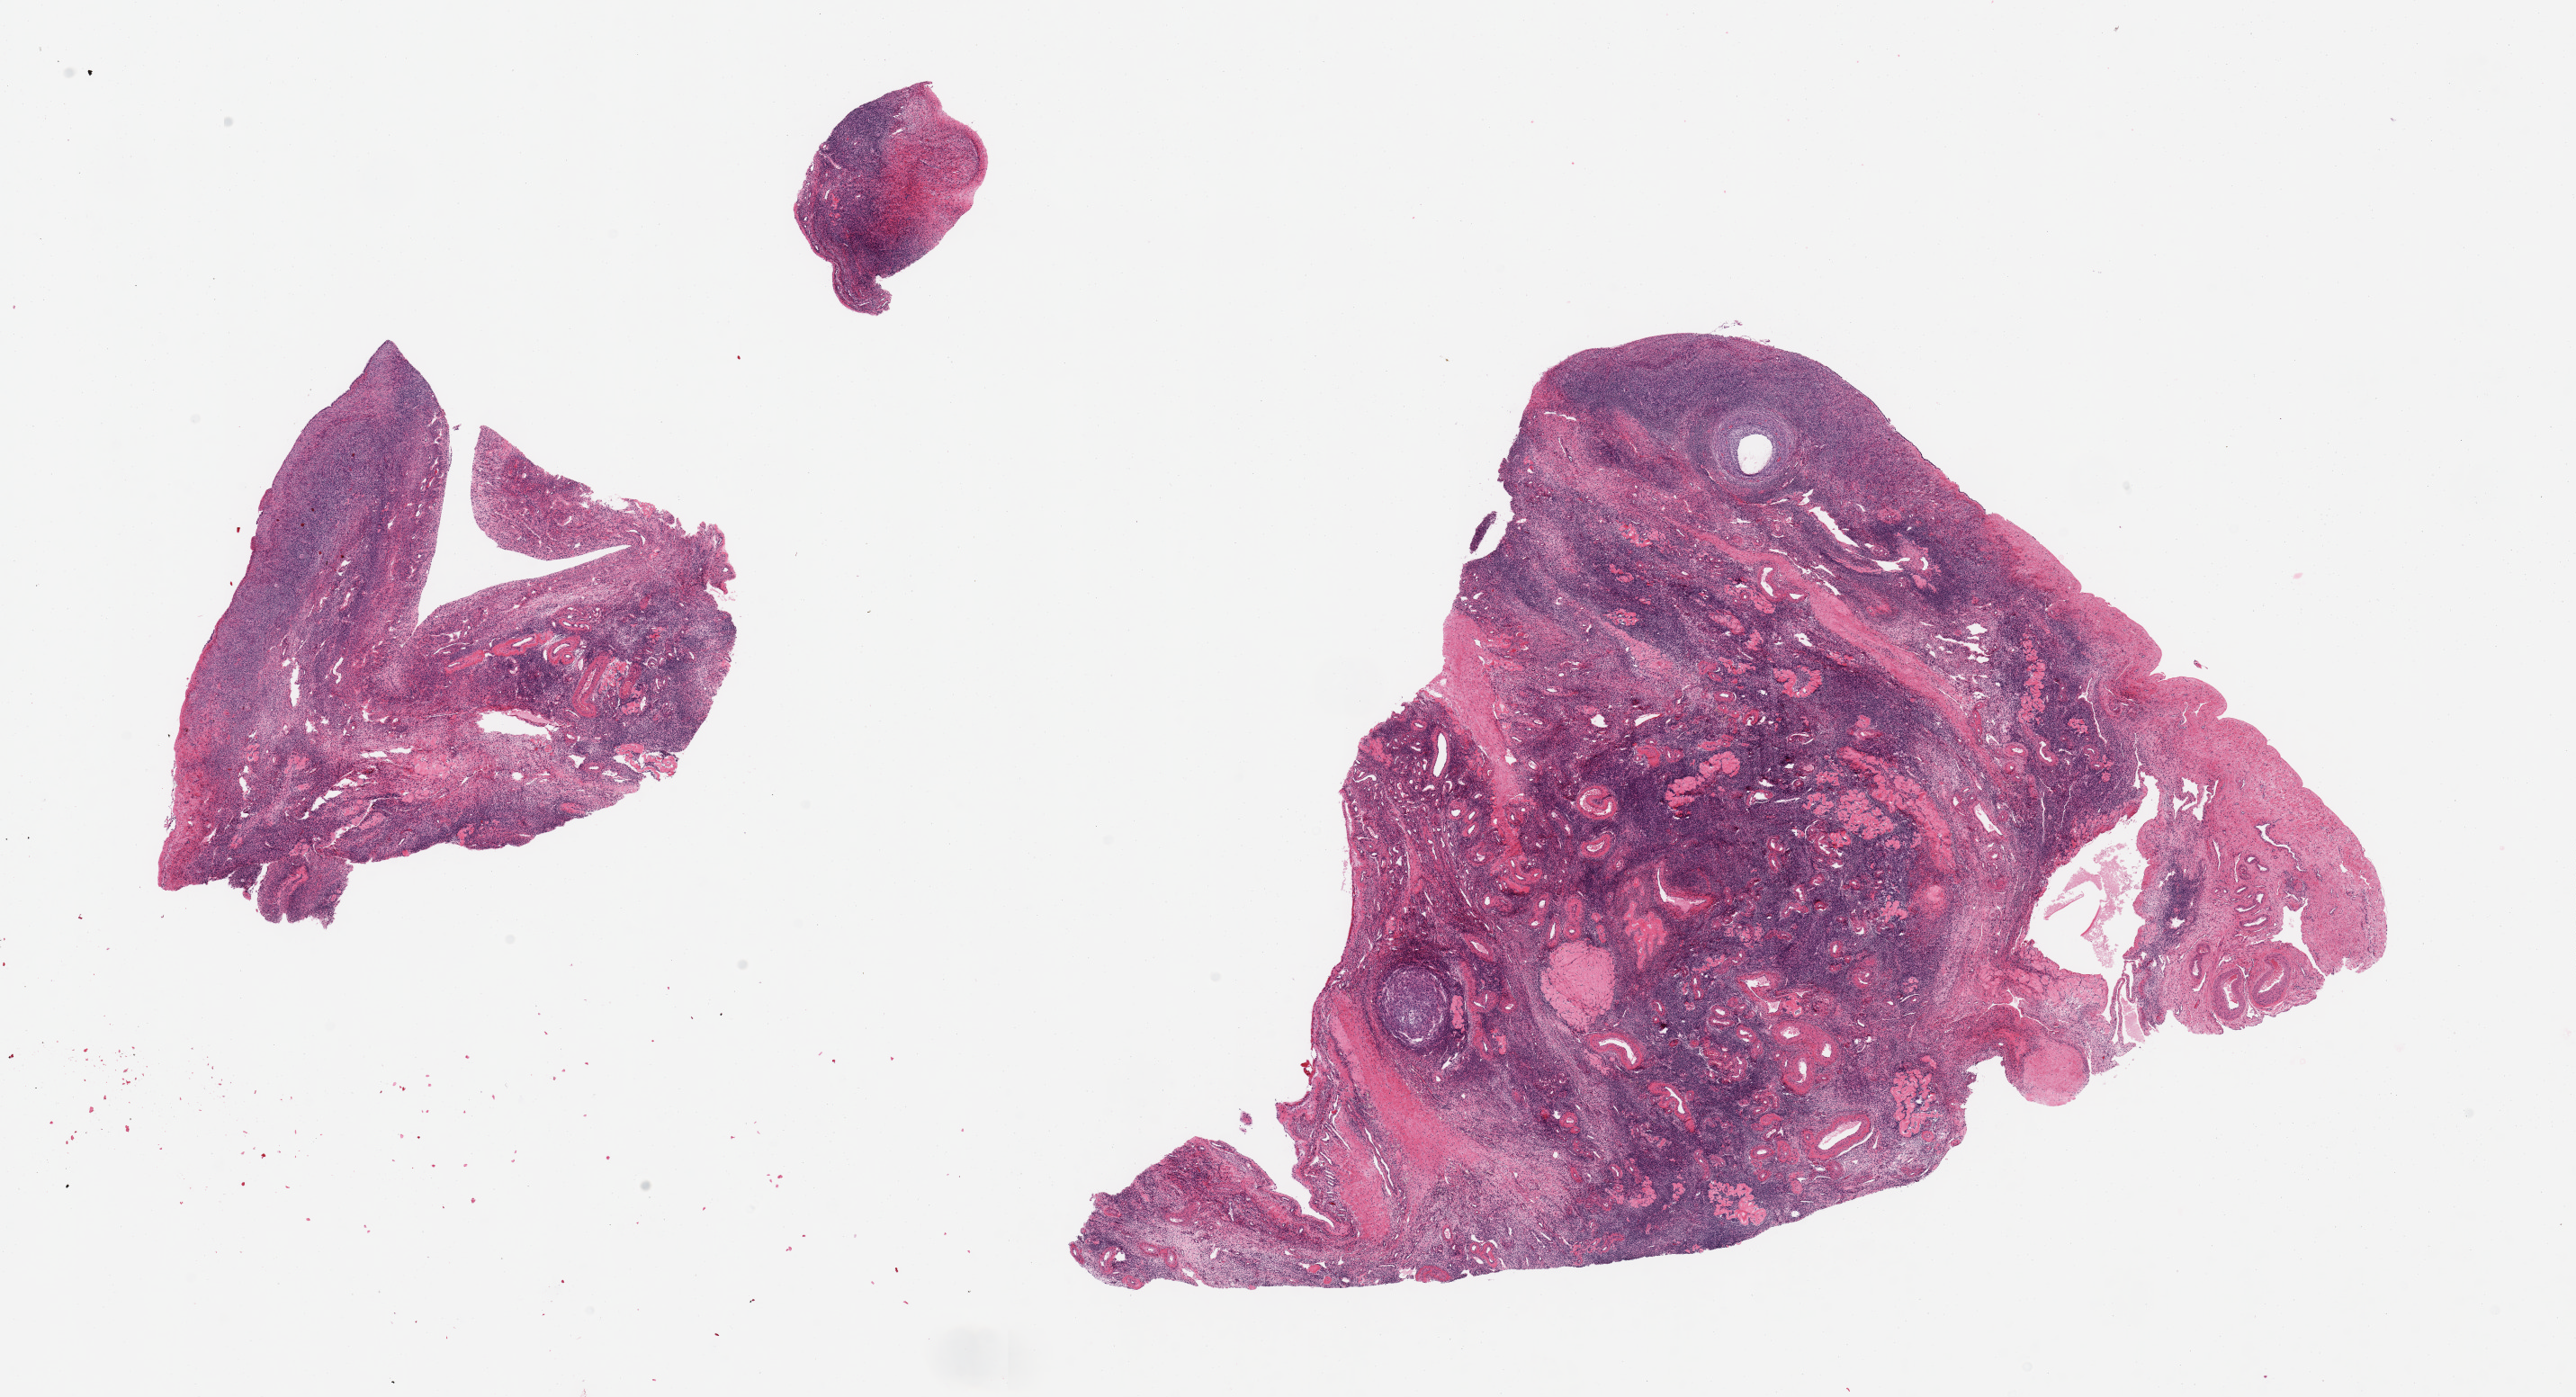
Digitized hematoxylin and eosin (H&E)-stained section — whole scanned area (about 22.6 x 12.3 mm) shown as a low-resolution overview; PAXgene-fixed, paraffin-embedded tissue; sampled site (target tissue): ovary; donor tissue sample. Donor sex: female.
Pathologist's review note for this sample: 2 pieces, atrophic cortex.